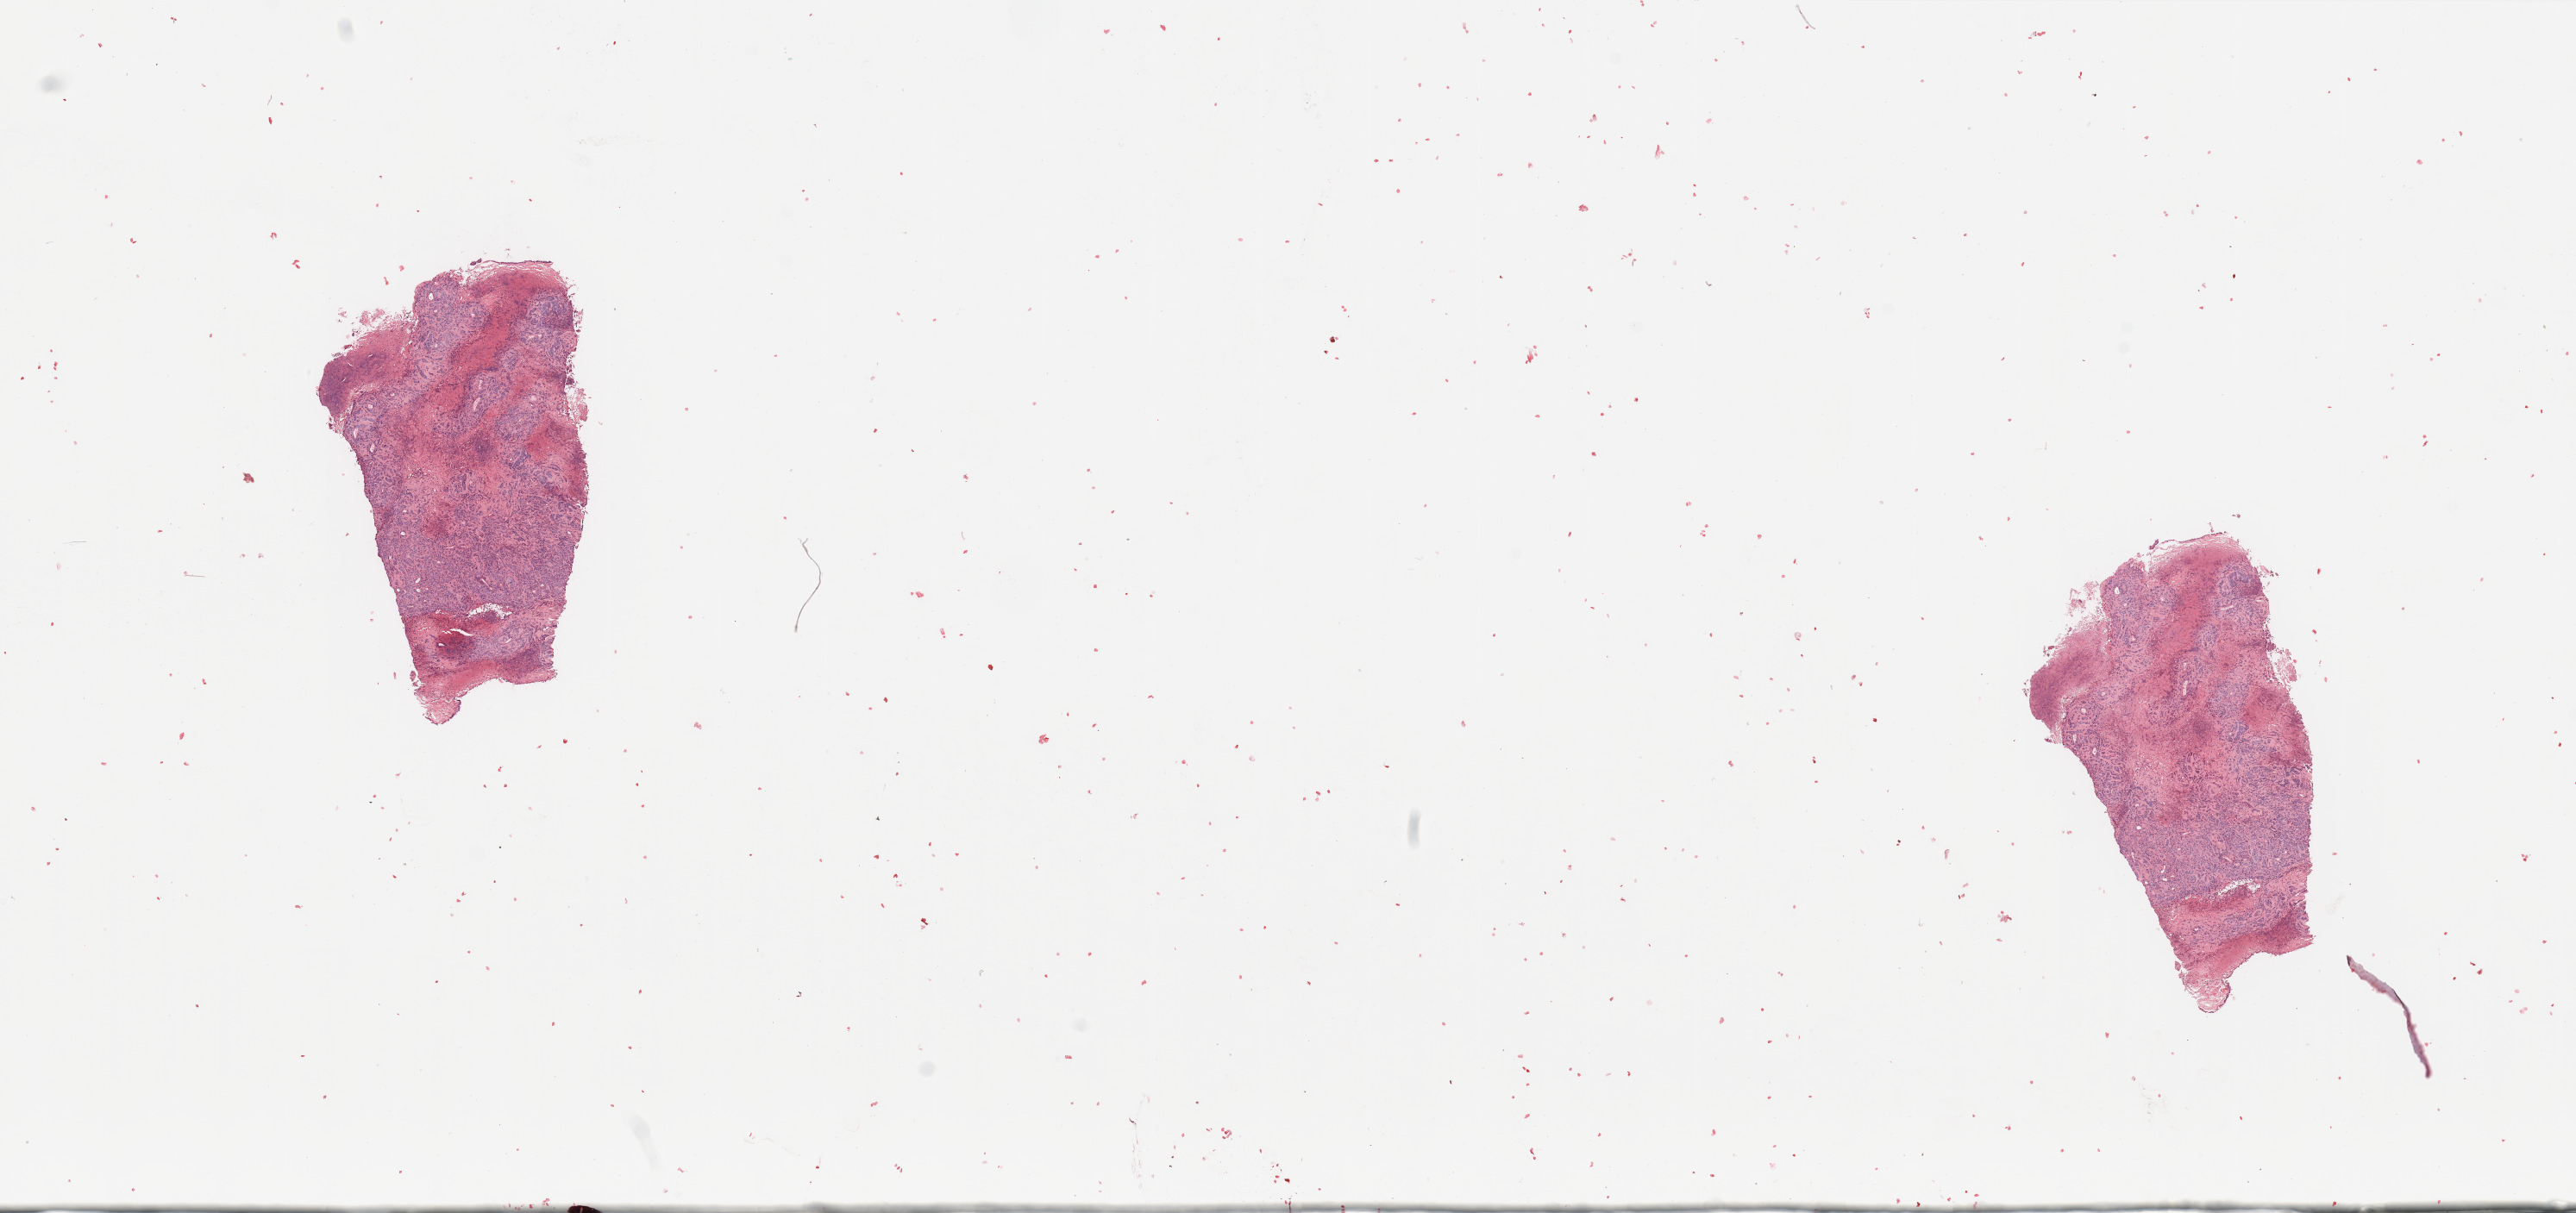
Whole-slide histology image, H&E — shown as a low-resolution overview of the whole scanned area (about 23.6 x 11.1 mm, slide scanned at 20x); uterus, tumour tissue. 73-year-old female patient. Histologic grade: G3 (poorly differentiated).
• AJCC pathologic stage: II
• histologic diagnosis: Endometrioid adenocarcinoma, NOS